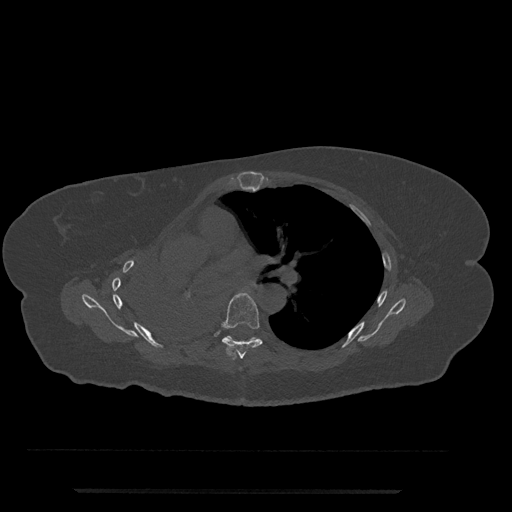
CT including the spine, one axial slice. Slice 489 of 797 in the series (ordered by position). Reconstruction kernel Br40s/3. 120 kVp. Bone window (W 1800 / L 400 HU). 0.5 mm slice thickness. 512 × 512 image matrix, field of view 440 × 440 mm. Female patient, age 51 years. Case-level facts recorded for this patient, not image findings: primary cancer: neuro; vertebrae with lytic lesions (as recorded): T8.
Annotated regions visible in this slice (semi-automatically segmented with operator editing):
- T6 vertebra: box from (x=222, y=292) to (x=263, y=359) px
- T7 vertebra: (x=227, y=336)–(x=257, y=341)